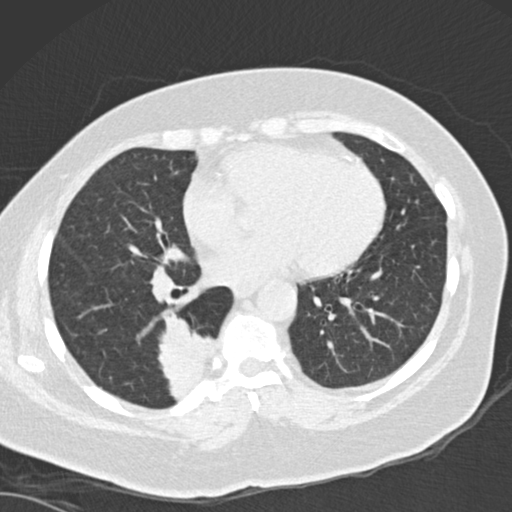
Low-dose screening chest CT, one axial slice. Reconstruction kernel B30f. Lung window (W 1500 / L -600 HU). 512 × 512 image matrix, field of view 328 × 328 mm.
Outlined on this slice (outlined manually by an expert reader):
- lesion 1 (tumor, lower lobe of right lung): bounding box (x1, y1, x2, y2) in pixels: (158, 311, 214, 401)